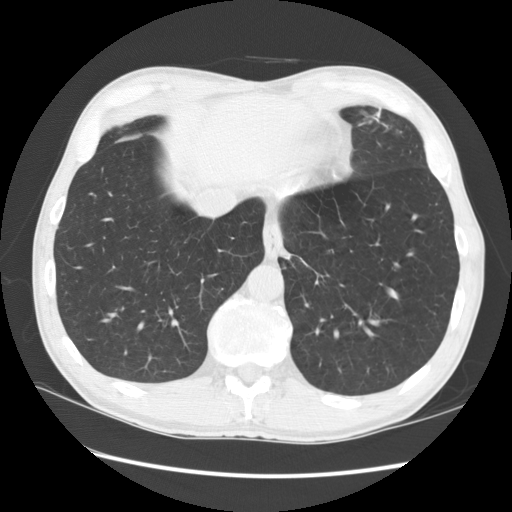
Low-dose screening chest CT, one axial slice; position 31 of 141 along the scan axis; reconstruction kernel STANDARD; 120 kVp; lung window (W 1500 / L -600 HU); 512 × 512 image matrix, field of view 360 × 360 mm.
Annotated regions visible in this slice (manually delineated by an expert):
- lesion 1 (tumor, lower lobe of left lung): bounding box [x1, y1, x2, y2] px = [373, 112, 378, 122]